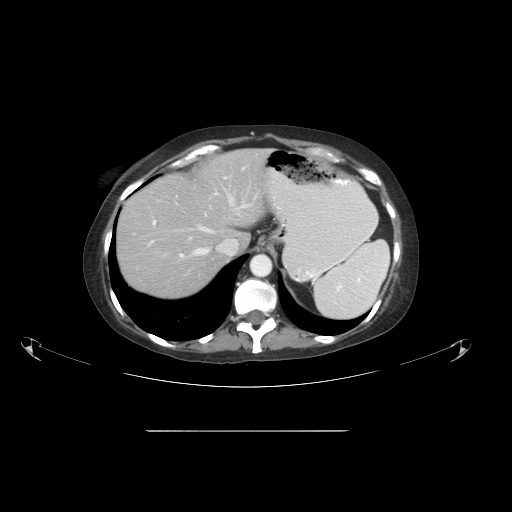
Contrast-enhanced abdominal CT, one axial slice; reconstruction kernel STANDARD; 120 kVp; intravenous contrast given; soft-tissue window (W 400 / L 40 HU); 5 mm slice thickness; 512 × 512 image matrix, field of view 475 × 475 mm. Female patient, age 48 years. From the clinical record (not read from this slice): diagnosis: colorectal cancer liver metastases, imaged before liver resection; multiple liver metastases: yes; largest metastasis: 1 cm.
Outlined on this slice (expert manual segmentation):
- hepatic veins: box from (x=193, y=194) to (x=251, y=255) px
- liver: (x=116, y=149)–(x=271, y=300)
- planned liver remnant (the part of the liver to remain after resection): (x=117, y=174)–(x=229, y=300)
- portal vein (with intrahepatic branches): (x=149, y=167)–(x=246, y=258)